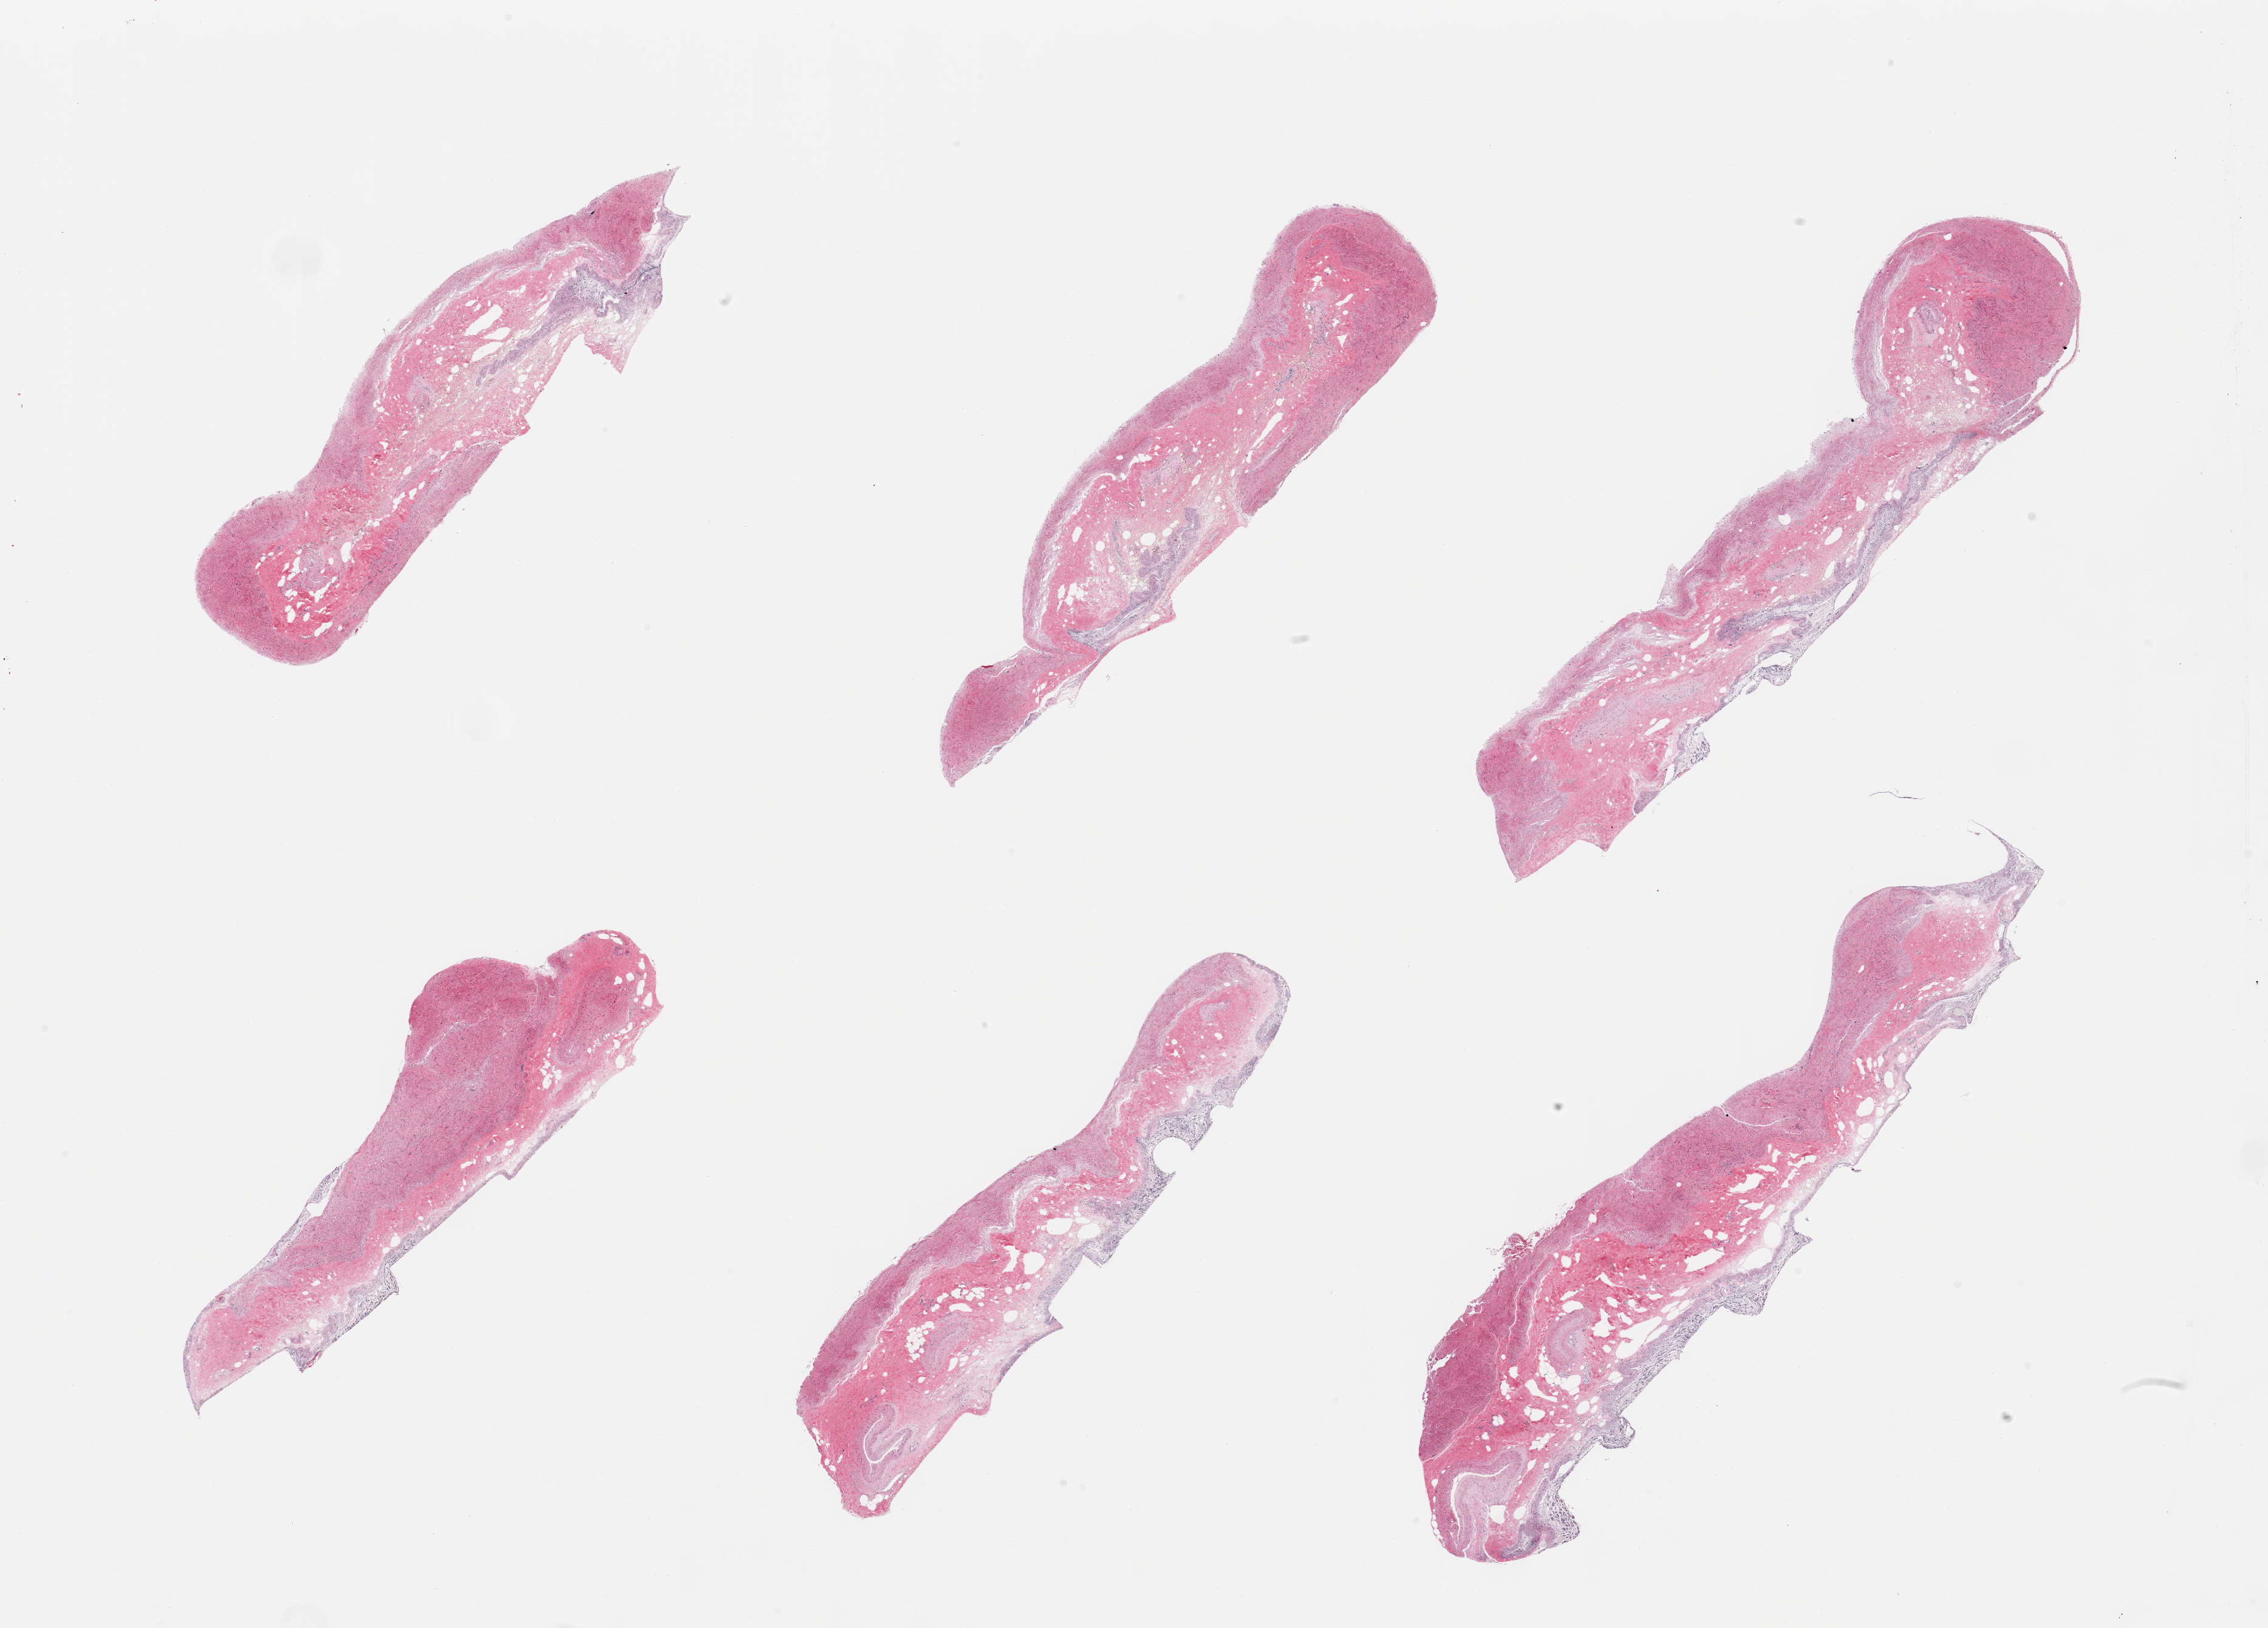
Digitized haematoxylin and eosin-stained section, a low-resolution overview of the entire scanned area, about 29.5 x 21.2 mm (from a 20x scan). PAXgene-fixed paraffin-embedded (PFPE) section. Sampled site (target tissue): stomach. Donor tissue sample. Donor sex: male.
Review note (as recorded): 6 pieces, mucosa with advanced autolysis or sloughed.